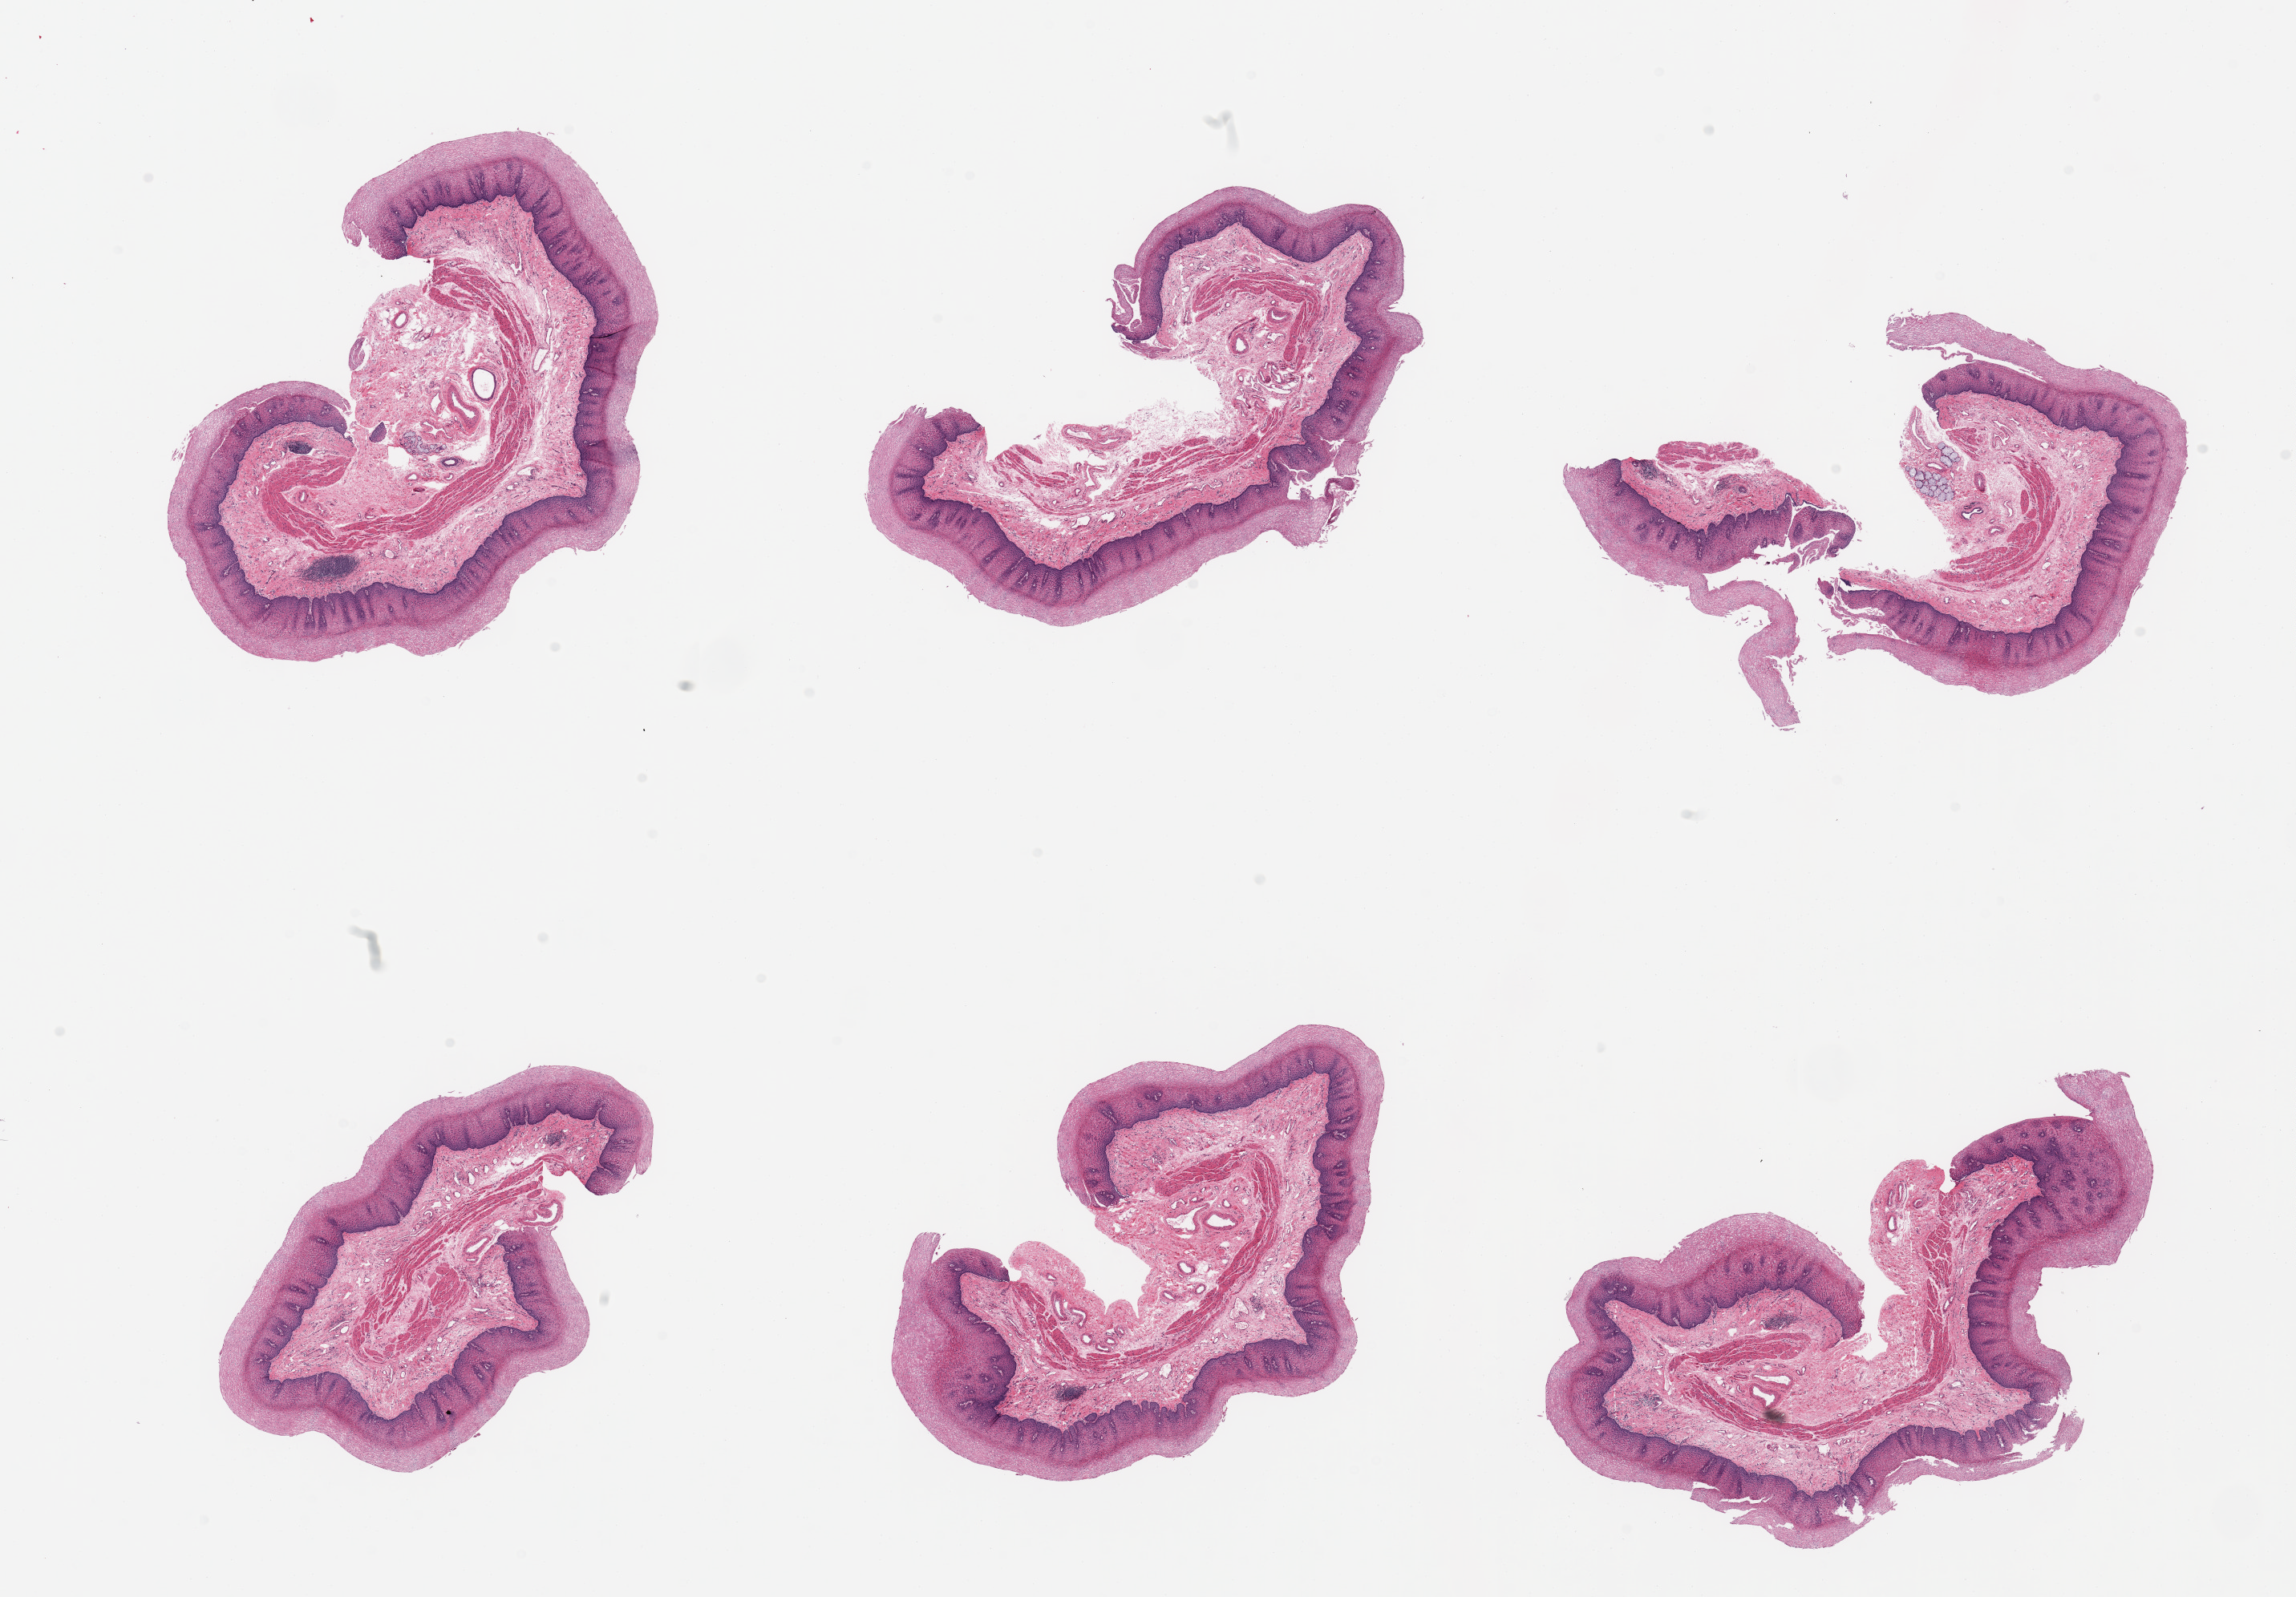
Whole-slide image, haematoxylin and eosin stain — low-resolution overview of the scanned area, about 22.6 x 15.8 mm. PAXgene-fixed paraffin-embedded (PFPE) section. Sampled site (target tissue): esophageal mucous membrane. Donor tissue sample. Donor: male.
* pathologist's review note for this sample: 6 pieces, squamous mucosa up to ~0.7mm, ~30% of thickness; Rare submucosal mucus glands present